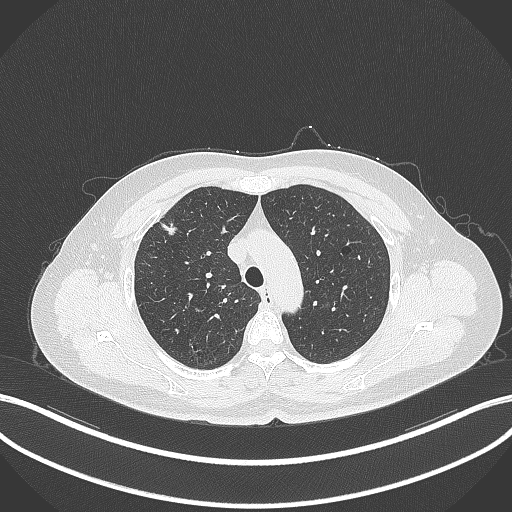
Chest CT, one axial slice; slice 274 of 353 in the series (ordered by position); reconstruction kernel B70f; 120 kVp; lung window (W 1500 / L -600 HU); 1 mm slice thickness; 512 × 512 image matrix, field of view 400 × 400 mm. Female patient, age 56 years. From the clinical record (not read from this slice): clinical TNM (as recorded): T1c N0 M0.
Structures marked on this image (rectangle marked by the reading radiologist):
- lung tumour (recorded histology: adenocarcinoma): bounding box (x1, y1, x2, y2) in pixels: (156, 216, 181, 237)